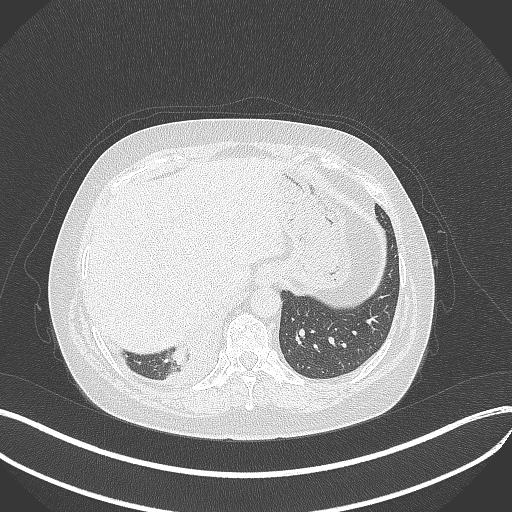
Chest CT, one axial slice; slice 73 of 381 in the series (ordered by position); reconstruction kernel B70f; lung window (W 1500 / L -600 HU); 1 mm slice thickness; 512 × 512 image matrix. Patient: female, 56 years. Case-level facts recorded for this patient, not image findings: clinical TNM (as recorded): T2b N1 M0.
Annotated regions visible in this slice (bounding box drawn by a radiologist):
- lung tumour (recorded histology: small cell carcinoma): bounding box (x1, y1, x2, y2) in pixels: (166, 339, 198, 371)